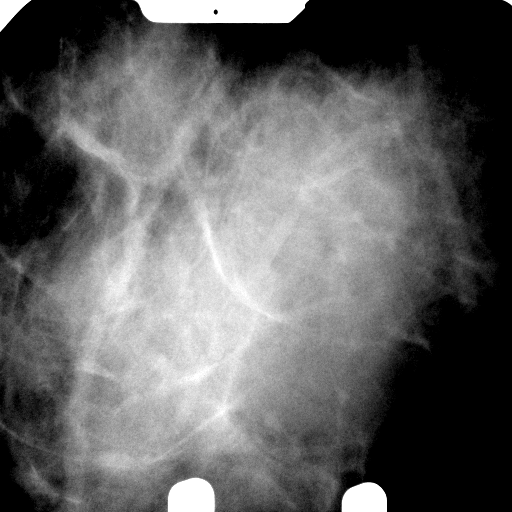
Spot-compression mammographic view.
Pathology recorded for this patient (not read from this image): pathology diagnosis: benign fibroadenoma (right breast); pathology report notes: RIGHT BREAST CALCIFICATION WITH NEEDLE LOCATION: FIBROADENOMA (1.9CM). REMAINING BREAST TISSUE WITH ADENOSIS, FOCAL FIBROADENOMATOUS CHANGES, APOCRINE METAPLASIA, FIBROCYSTIC CHANGES, SMALL INTRADUCTAL PAPILLOMAS, AND USUAL TYPE DUCTAL HYPERPLASIA. MICROCALCIFICATIONS ASSOCIATED WITH BENIGN BREAST TISSUE ARE IDENTIFIED. NO IN-SITU OR INVASIVE CARCINOMA.